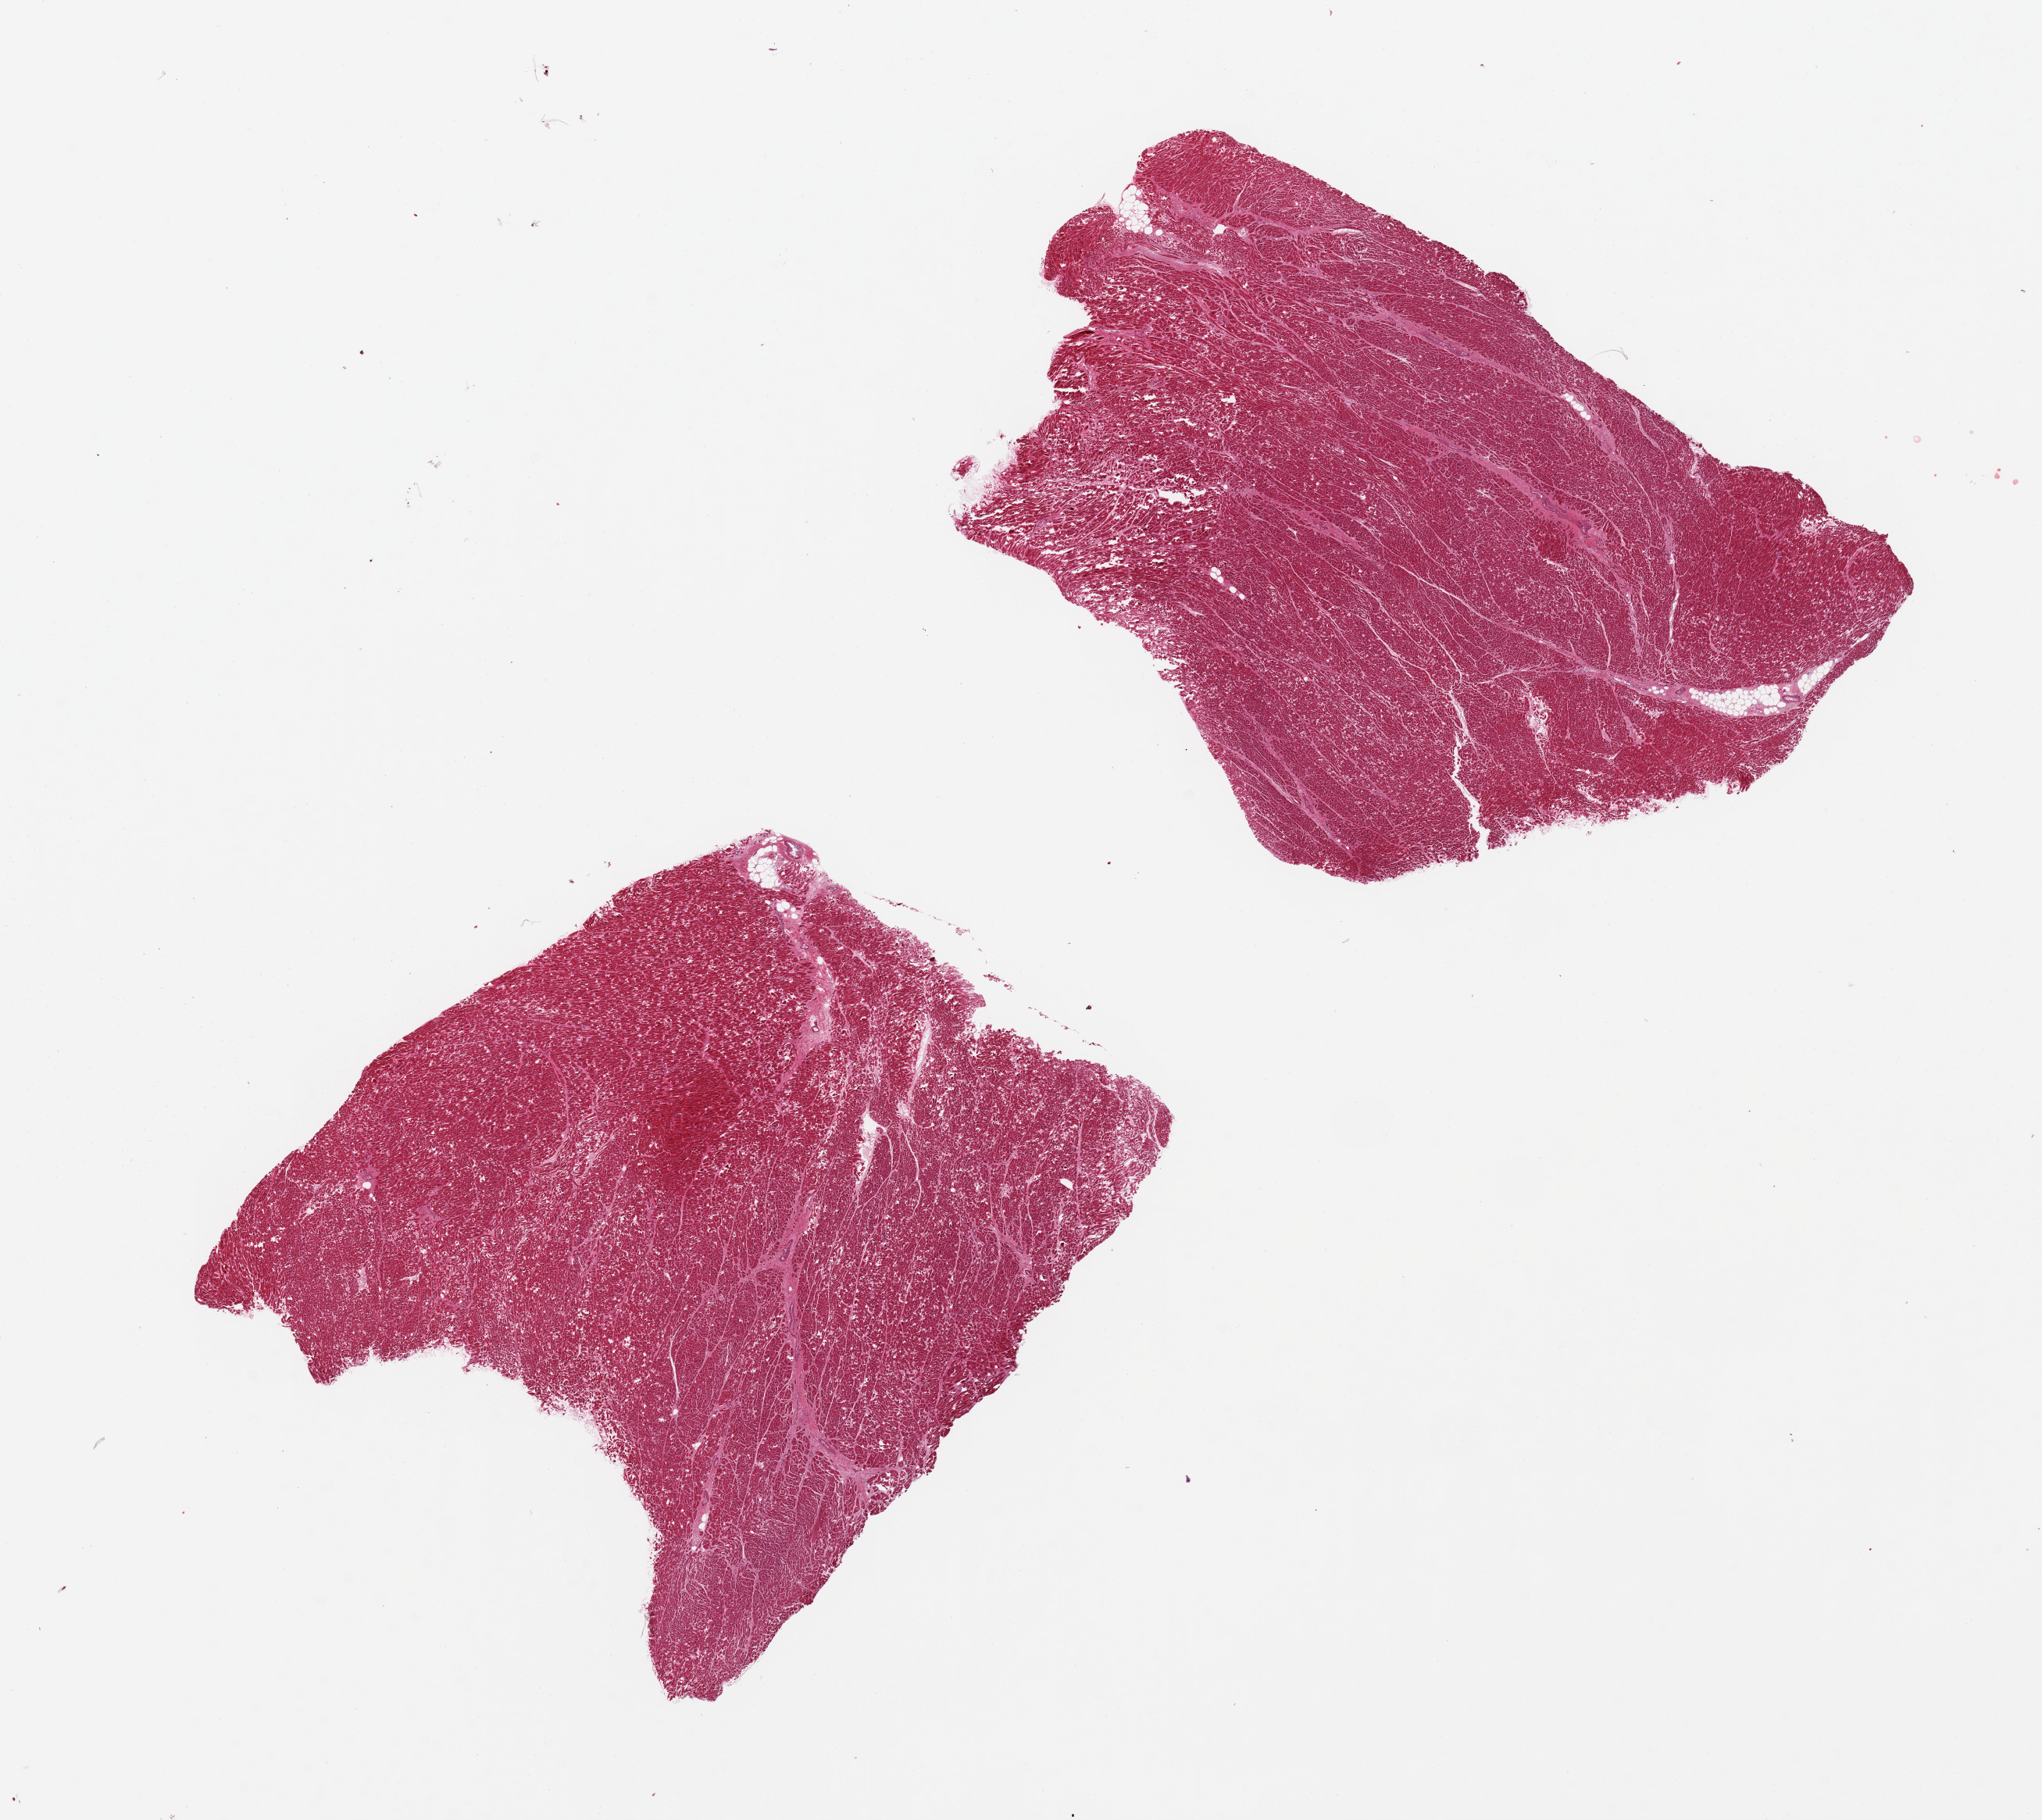
Haematoxylin and eosin whole-slide image, brightfield — low-resolution overview of the scanned area, about 20.7 x 18.4 mm. PAXgene-fixed, paraffin-embedded tissue. Sampled site (target tissue): heart. Tissue donor sample. Female donor.
• pathologist's review note for this sample: 2 pieces mild ischemic changes (subacute, 'boxcar nuclei')